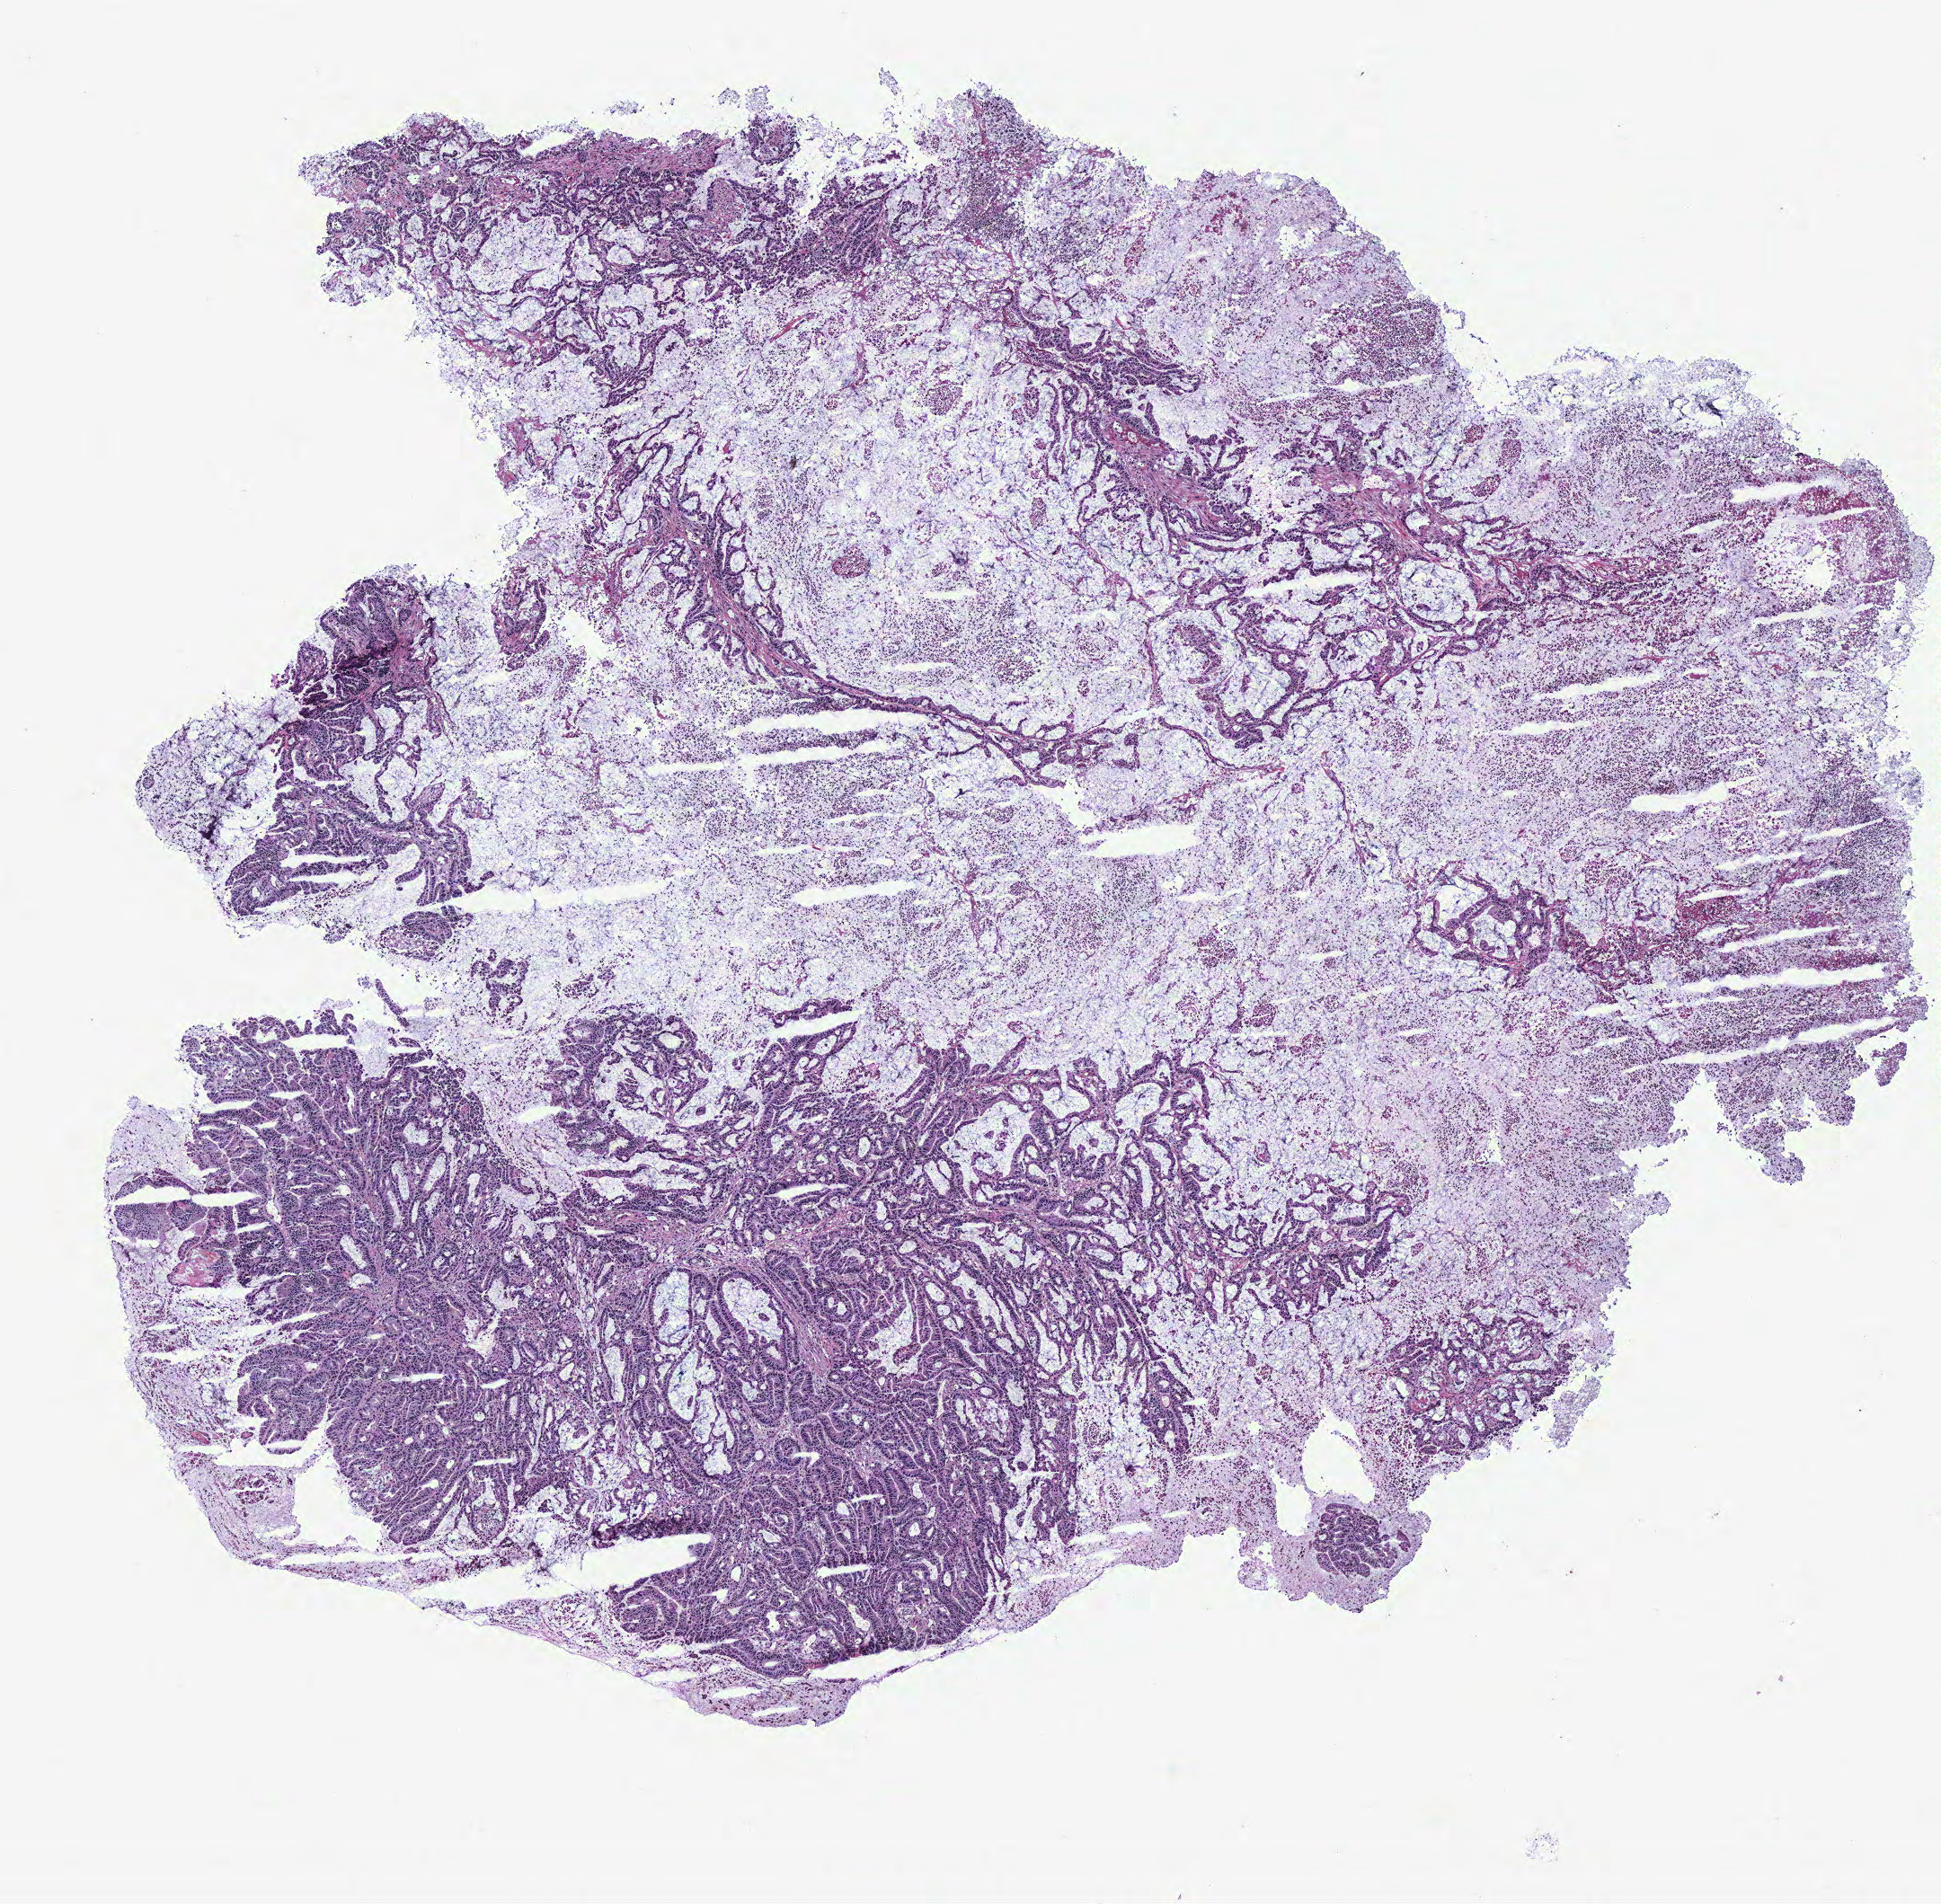
Whole-slide histology image, H&E, whole scanned area (about 8.6 x 8.5 mm, slide scanned at 40x) shown as a low-resolution overview. Colon, normal (non-tumour) tissue. Patient: female, age 77 years.
• this section: normal (non-tumour) tissue from the same patient
• patient diagnosis: Adenocarcinoma, NOS